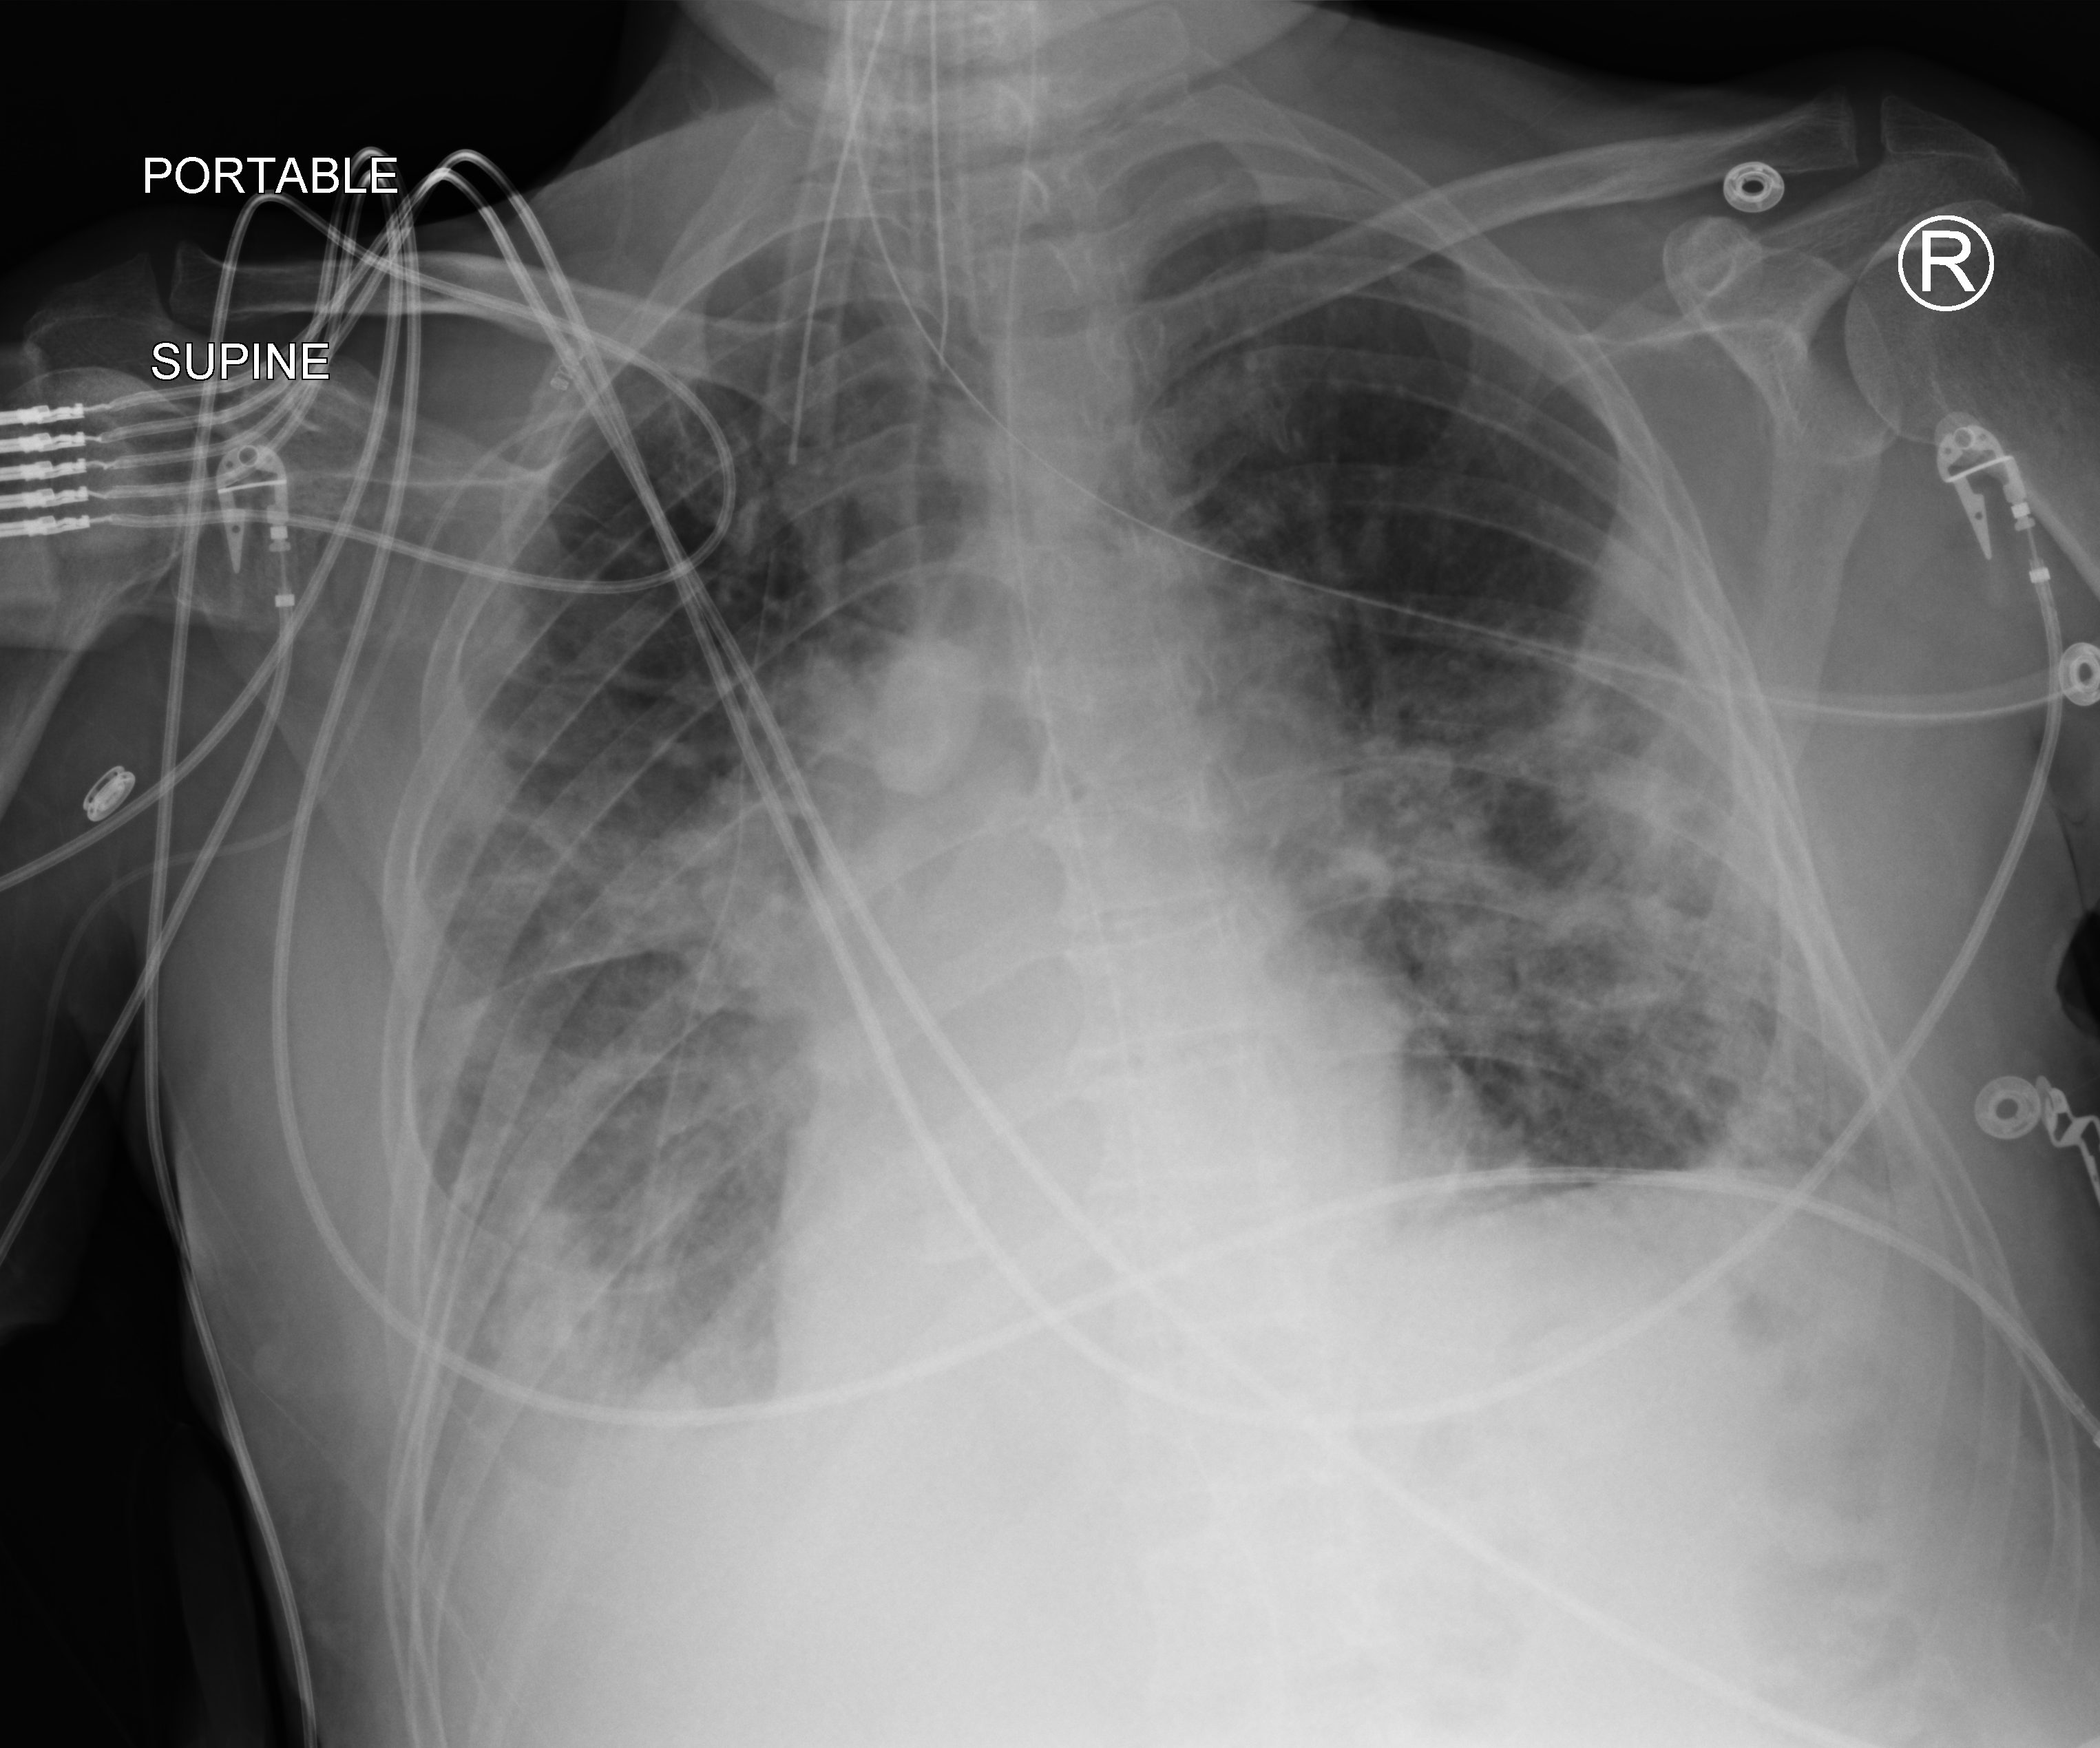
Portable chest radiograph, anteroposterior (AP) projection. Patient hospitalised with COVID-19; male, aged 75–90 years.
From the hospital-stay record, not from the radiograph (when in the stay this image was taken is not recorded): admitted to intensive care during this hospital stay: yes; mechanically ventilated during this hospital stay: yes.